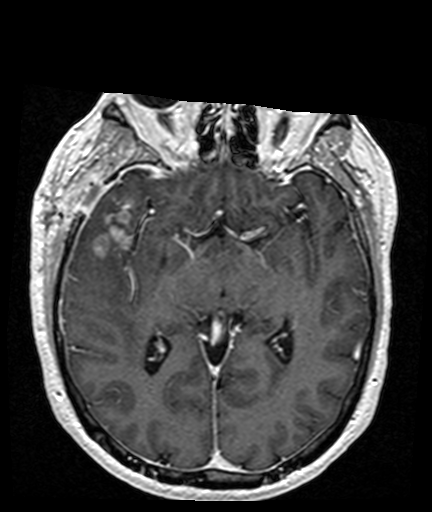
Brain MRI from a brain-tumour surgery series, one axial slice; position 94 of 176 along the scan axis; T1-weighted post-contrast; 1 mm slice thickness; 432 × 512 image matrix, field of view 194 × 230 mm. From the clinical record (not read from this slice): histopathology: Glioblastoma; WHO grade: 4; IDH mutation: no; tumour location: Right Frontal Temporal, Posterior Sylvian Fissure.
Annotated regions visible in this slice (outlined manually by an expert reader):
- tumour: bounding box [x1, y1, x2, y2] px = [95, 202, 136, 258]